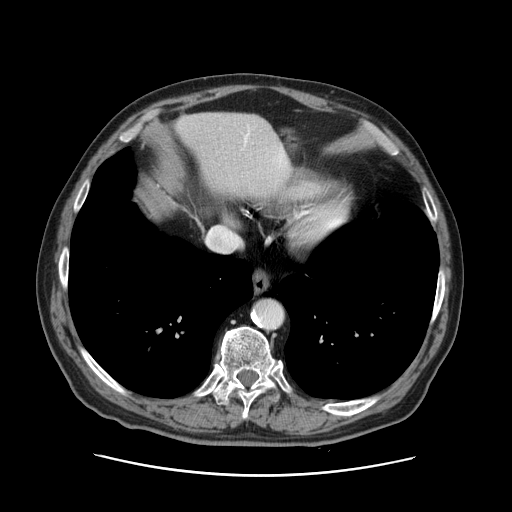
Contrast-enhanced abdominal CT, one axial slice; slice 119 of 141 in the series (ordered by position); soft-tissue window (W 400 / L 40 HU); 2.5 mm slice thickness; 512 × 512 image matrix, field of view 395 × 395 mm. Male patient, age 72 years. From the clinical record (not read from this slice): diagnosis: colorectal cancer liver metastases, imaged before liver resection; multiple liver metastases: yes; largest metastasis: 5.4 cm; disease in both lobes: yes.
Annotated regions visible in this slice (expert manual segmentation):
- hepatic veins: bounding box (x1, y1, x2, y2) in pixels: (244, 130, 250, 147)
- liver: (176, 113, 288, 195)
- planned liver remnant (the part of the liver to remain after resection): (176, 113, 289, 195)